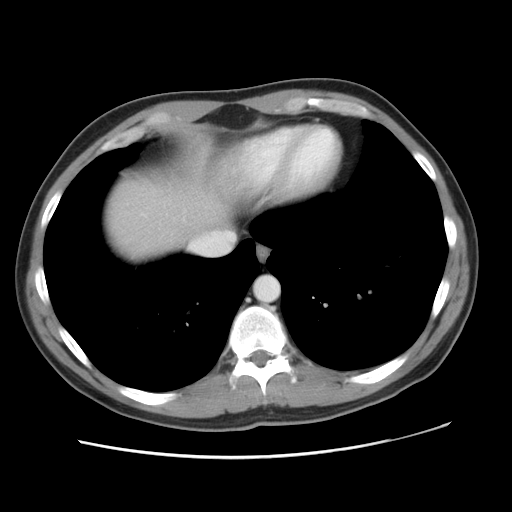
Contrast-enhanced abdominal CT, one axial slice. Slice 44 of 49 in the series (ordered by position). Reconstruction kernel STANDARD. 120 kVp. Soft-tissue window (W 400 / L 40 HU). 5 mm slice thickness. 512 × 512 image matrix. Male patient, age 41 years. Case-level facts recorded for this patient, not image findings: diagnosis: colorectal cancer liver metastases, imaged before liver resection; multiple liver metastases: yes.
Annotated regions visible in this slice (manually delineated by an expert):
- liver: bounding box (x1, y1, x2, y2) in pixels: (105, 152, 227, 262)
- planned liver remnant (the part of the liver to remain after resection): (124, 152, 227, 233)
- portal vein (with intrahepatic branches): (214, 231, 216, 233)